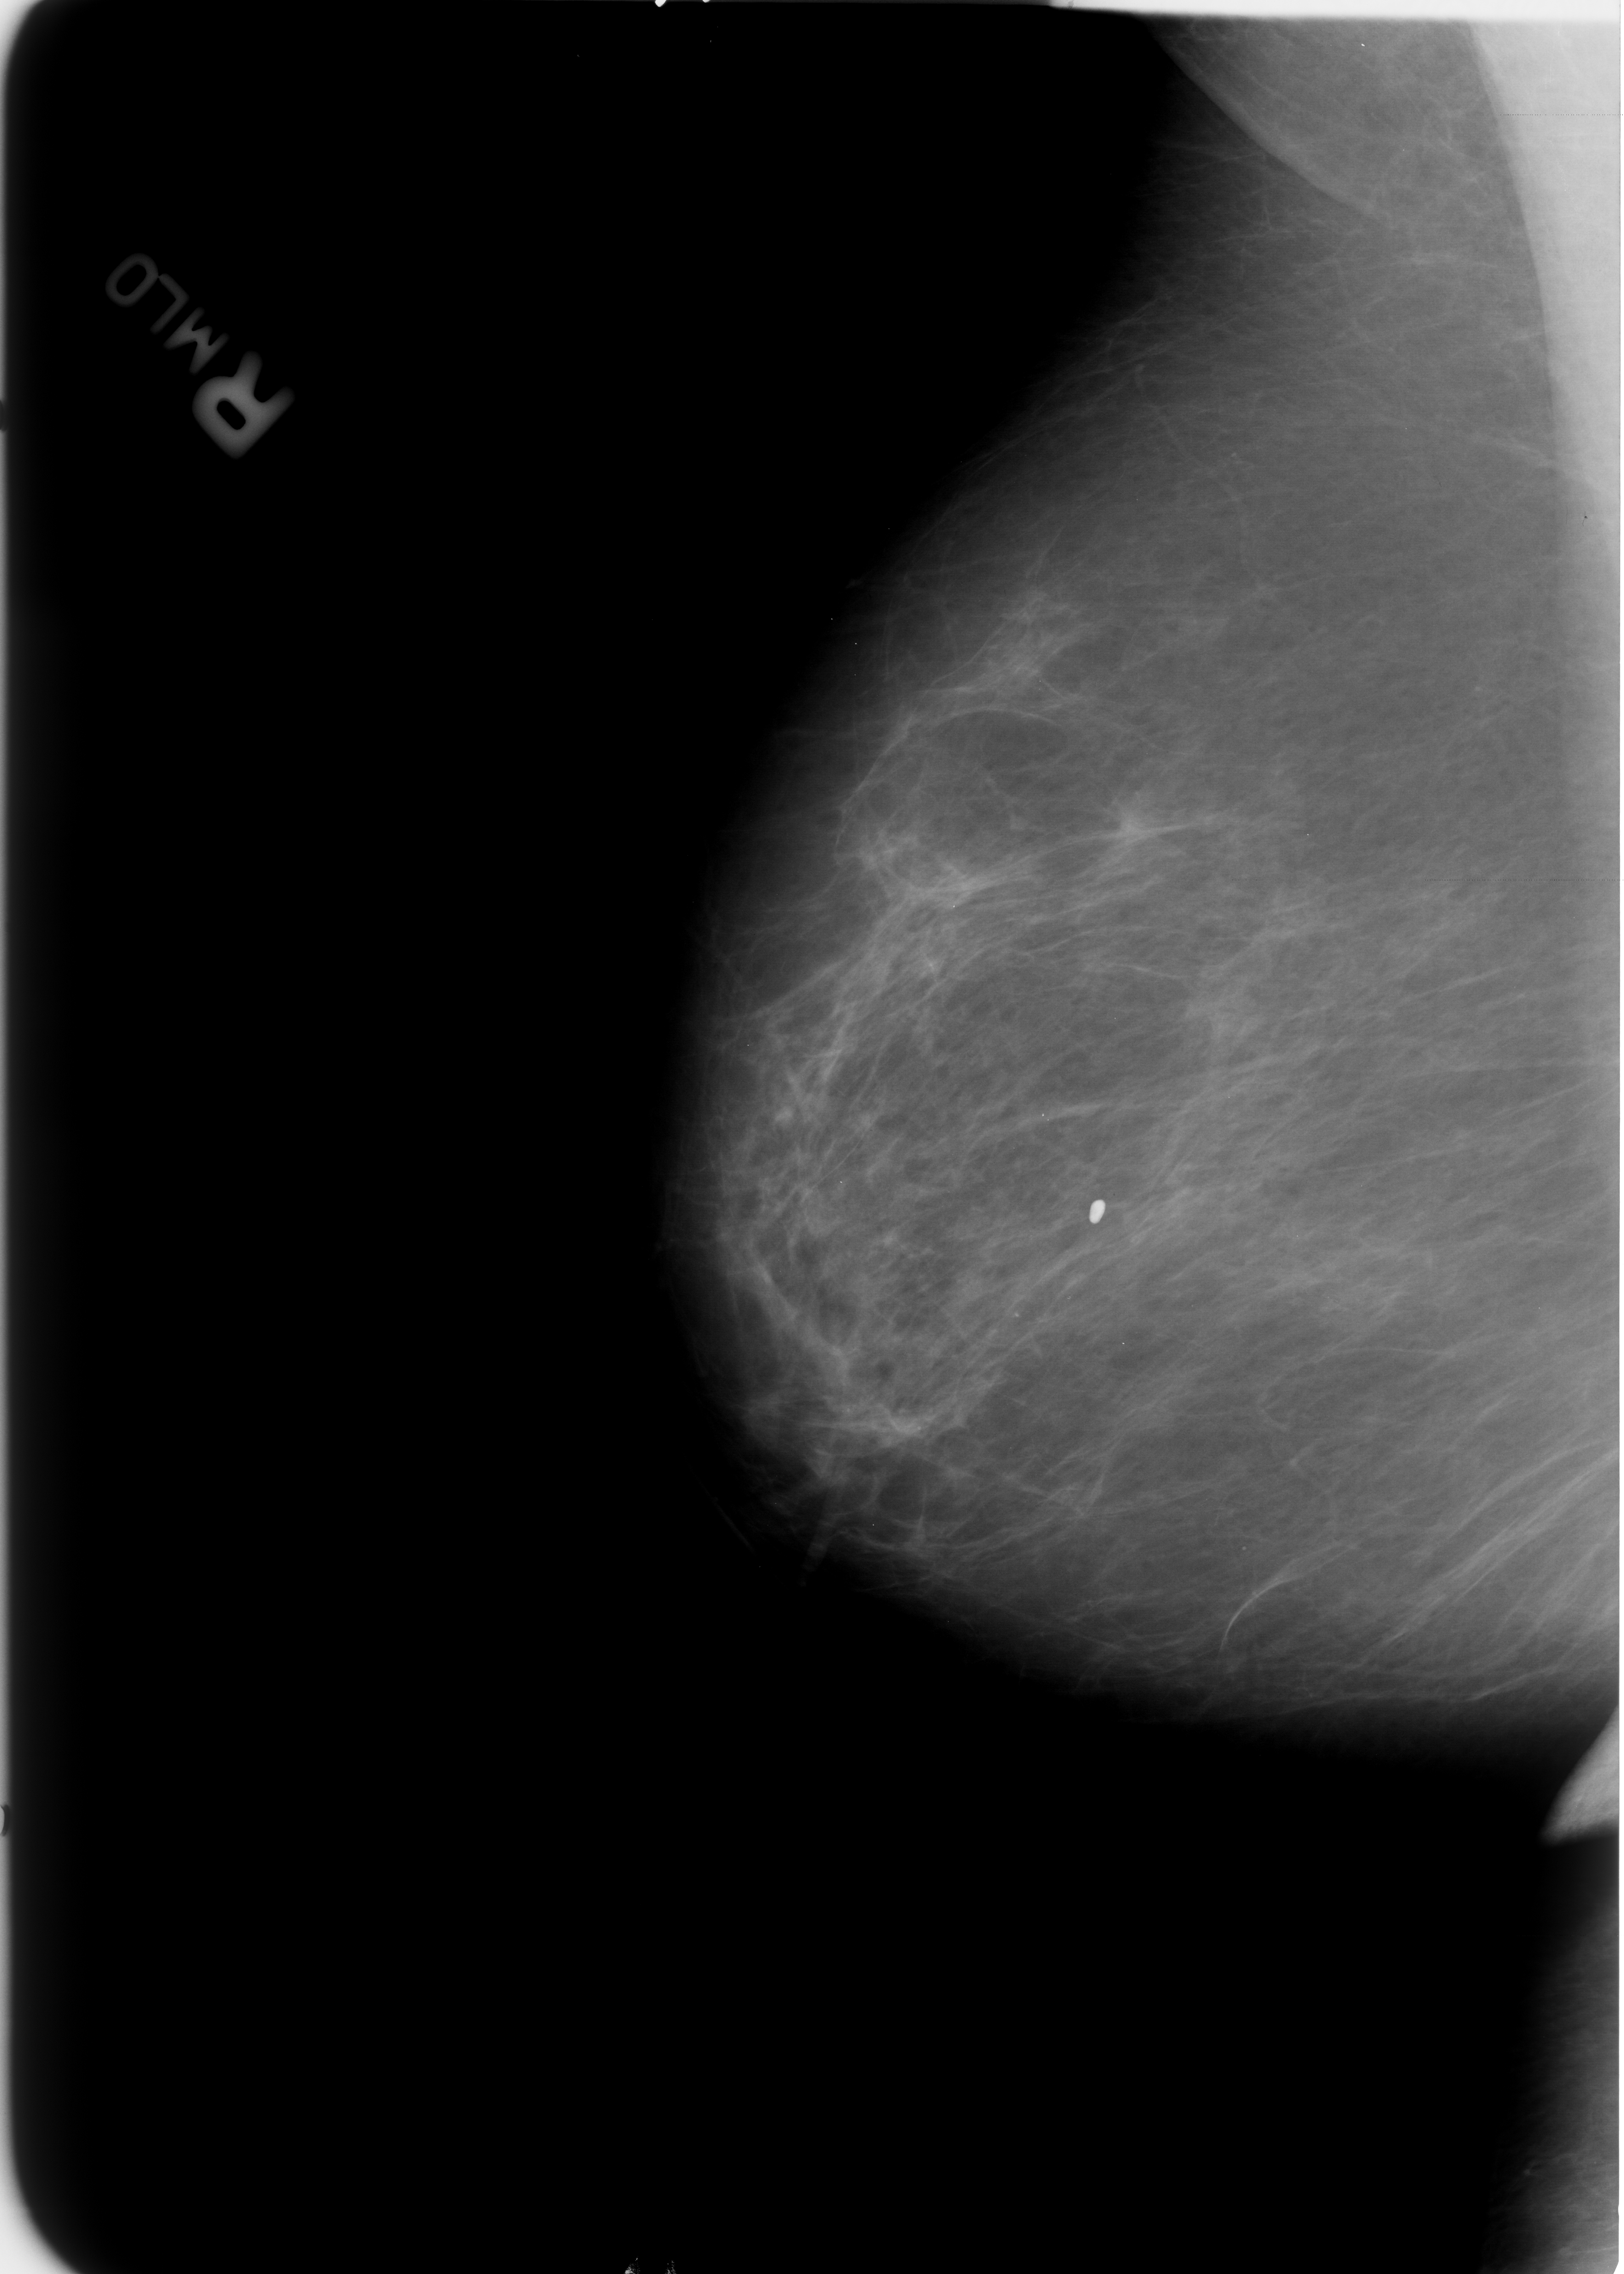
Scanned film-screen mammogram; right breast; MLO view; 1624 × 2274 image matrix.
Marked abnormalities (boxes around the expert regions of interest):
- calcifications, morphology coarse; BI-RADS assessment category 2; benign; no additional work-up was recommended (outcome (as recorded, no biopsy): benign without callback): bounding box <1079,1194,1119,1233> (left, top, right, bottom; pixels)